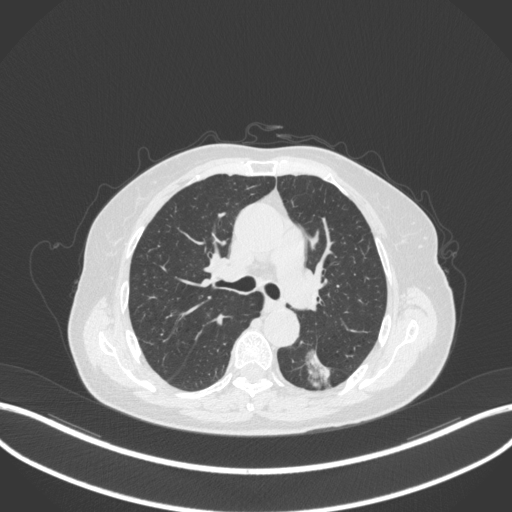
Chest CT, one axial slice. Position 191 of 352 along the scan axis. Reconstruction kernel B31f. 120 kVp. Lung window (W 1500 / L -600 HU). 1 mm slice thickness. 512 × 512 image matrix. Patient: female, 70 years. From the clinical record (not read from this slice): clinical TNM (as recorded): T1c N0 M0.
Outlined on this slice (bounding box drawn by a radiologist):
- lung tumour (recorded histology: adenocarcinoma): box from (x=302, y=342) to (x=333, y=389) px